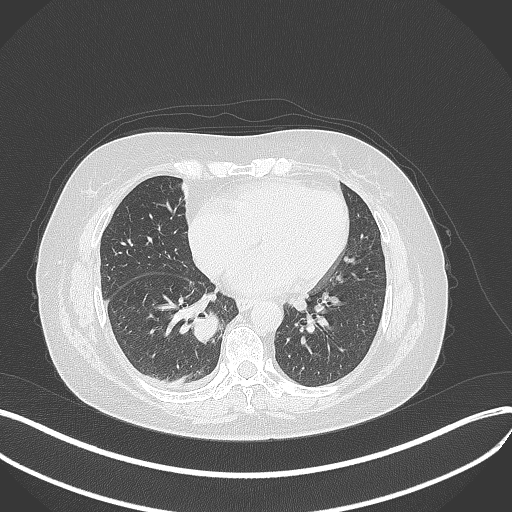
Chest CT, one axial slice. Slice 142 of 381 in the series (ordered by position). 120 kVp. Lung window (W 1500 / L -600 HU). 1 mm slice thickness. 512 × 512 image matrix, field of view 400 × 400 mm. Female patient, age 56 years. Case-level facts recorded for this patient, not image findings: clinical TNM (as recorded): T2b N1 M0; histopathological grade: G3.
Annotated regions visible in this slice (bounding box drawn by a radiologist):
- lung tumour (recorded histology: small cell carcinoma): bounding box (x1, y1, x2, y2) in pixels: (190, 310, 223, 350)